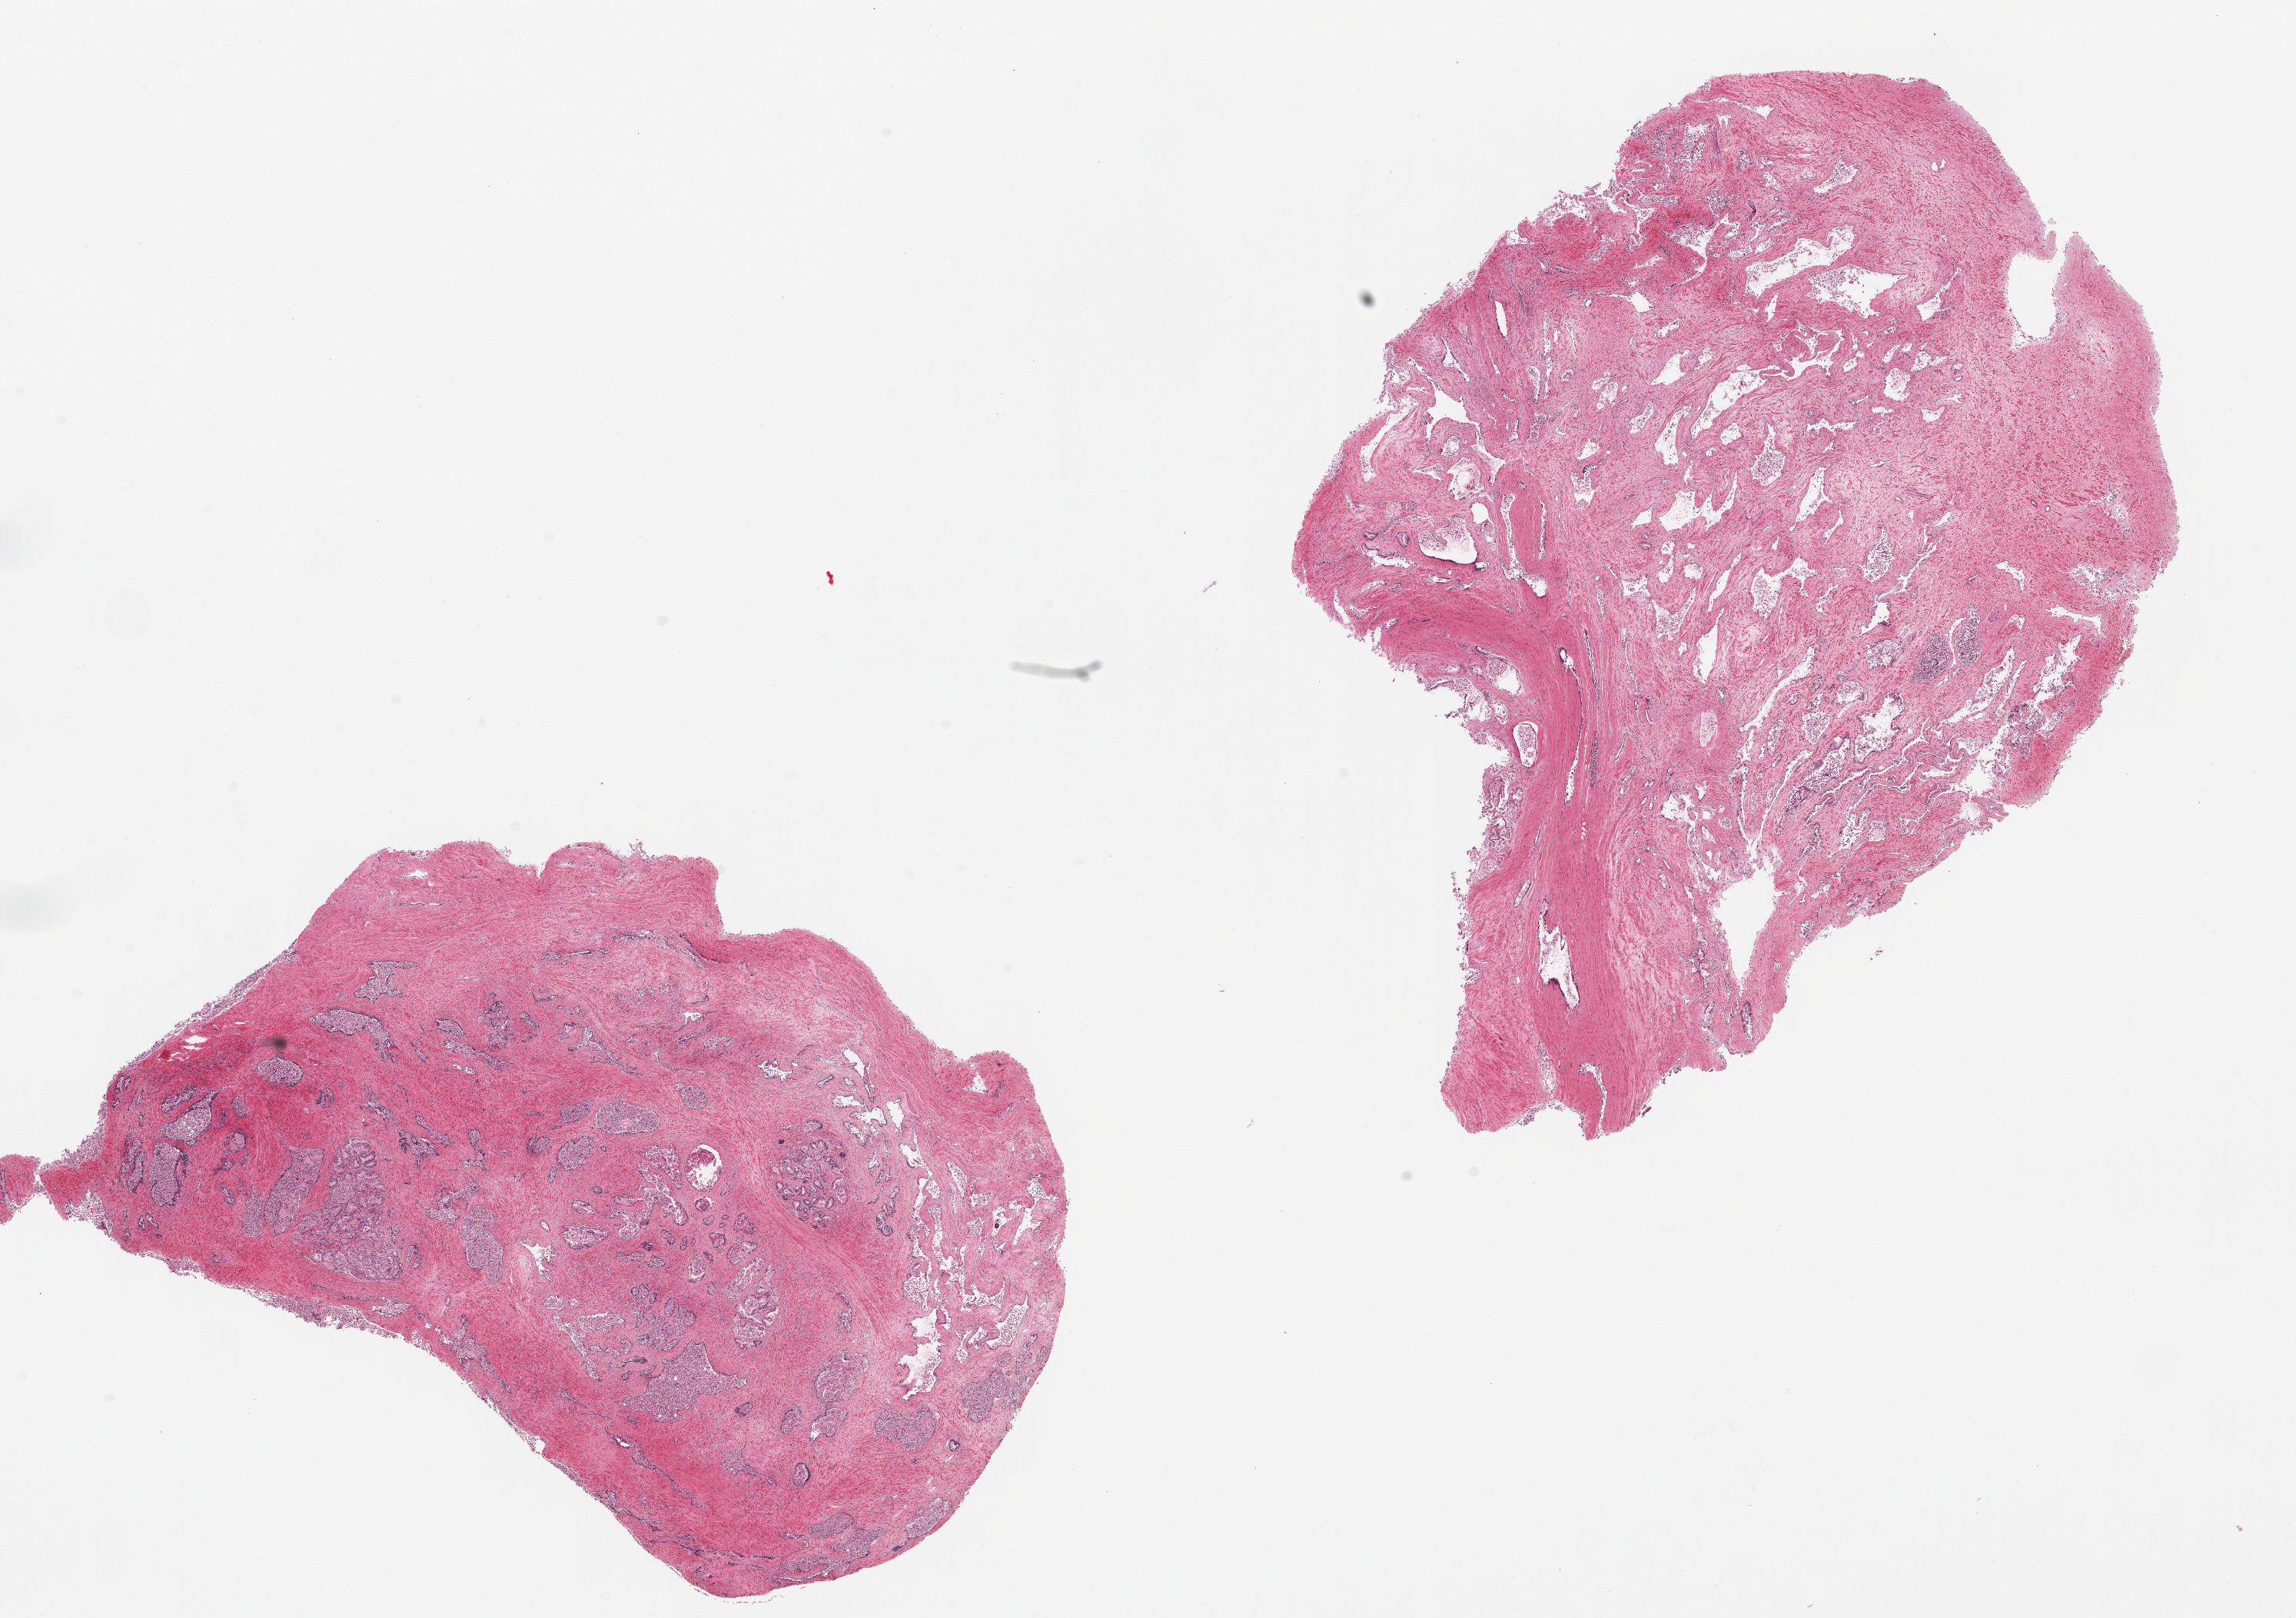
H&E whole-slide image — low-resolution overview of the scanned area, about 23.6 x 16.6 mm; PAXgene-fixed, paraffin-embedded tissue; section of prostate (target tissue); tissue donor sample. Donor sex: male.
* pathologist's review note for this sample: 2 pieces, glandular hyperplasia pattern, mucosa toally autolyzed